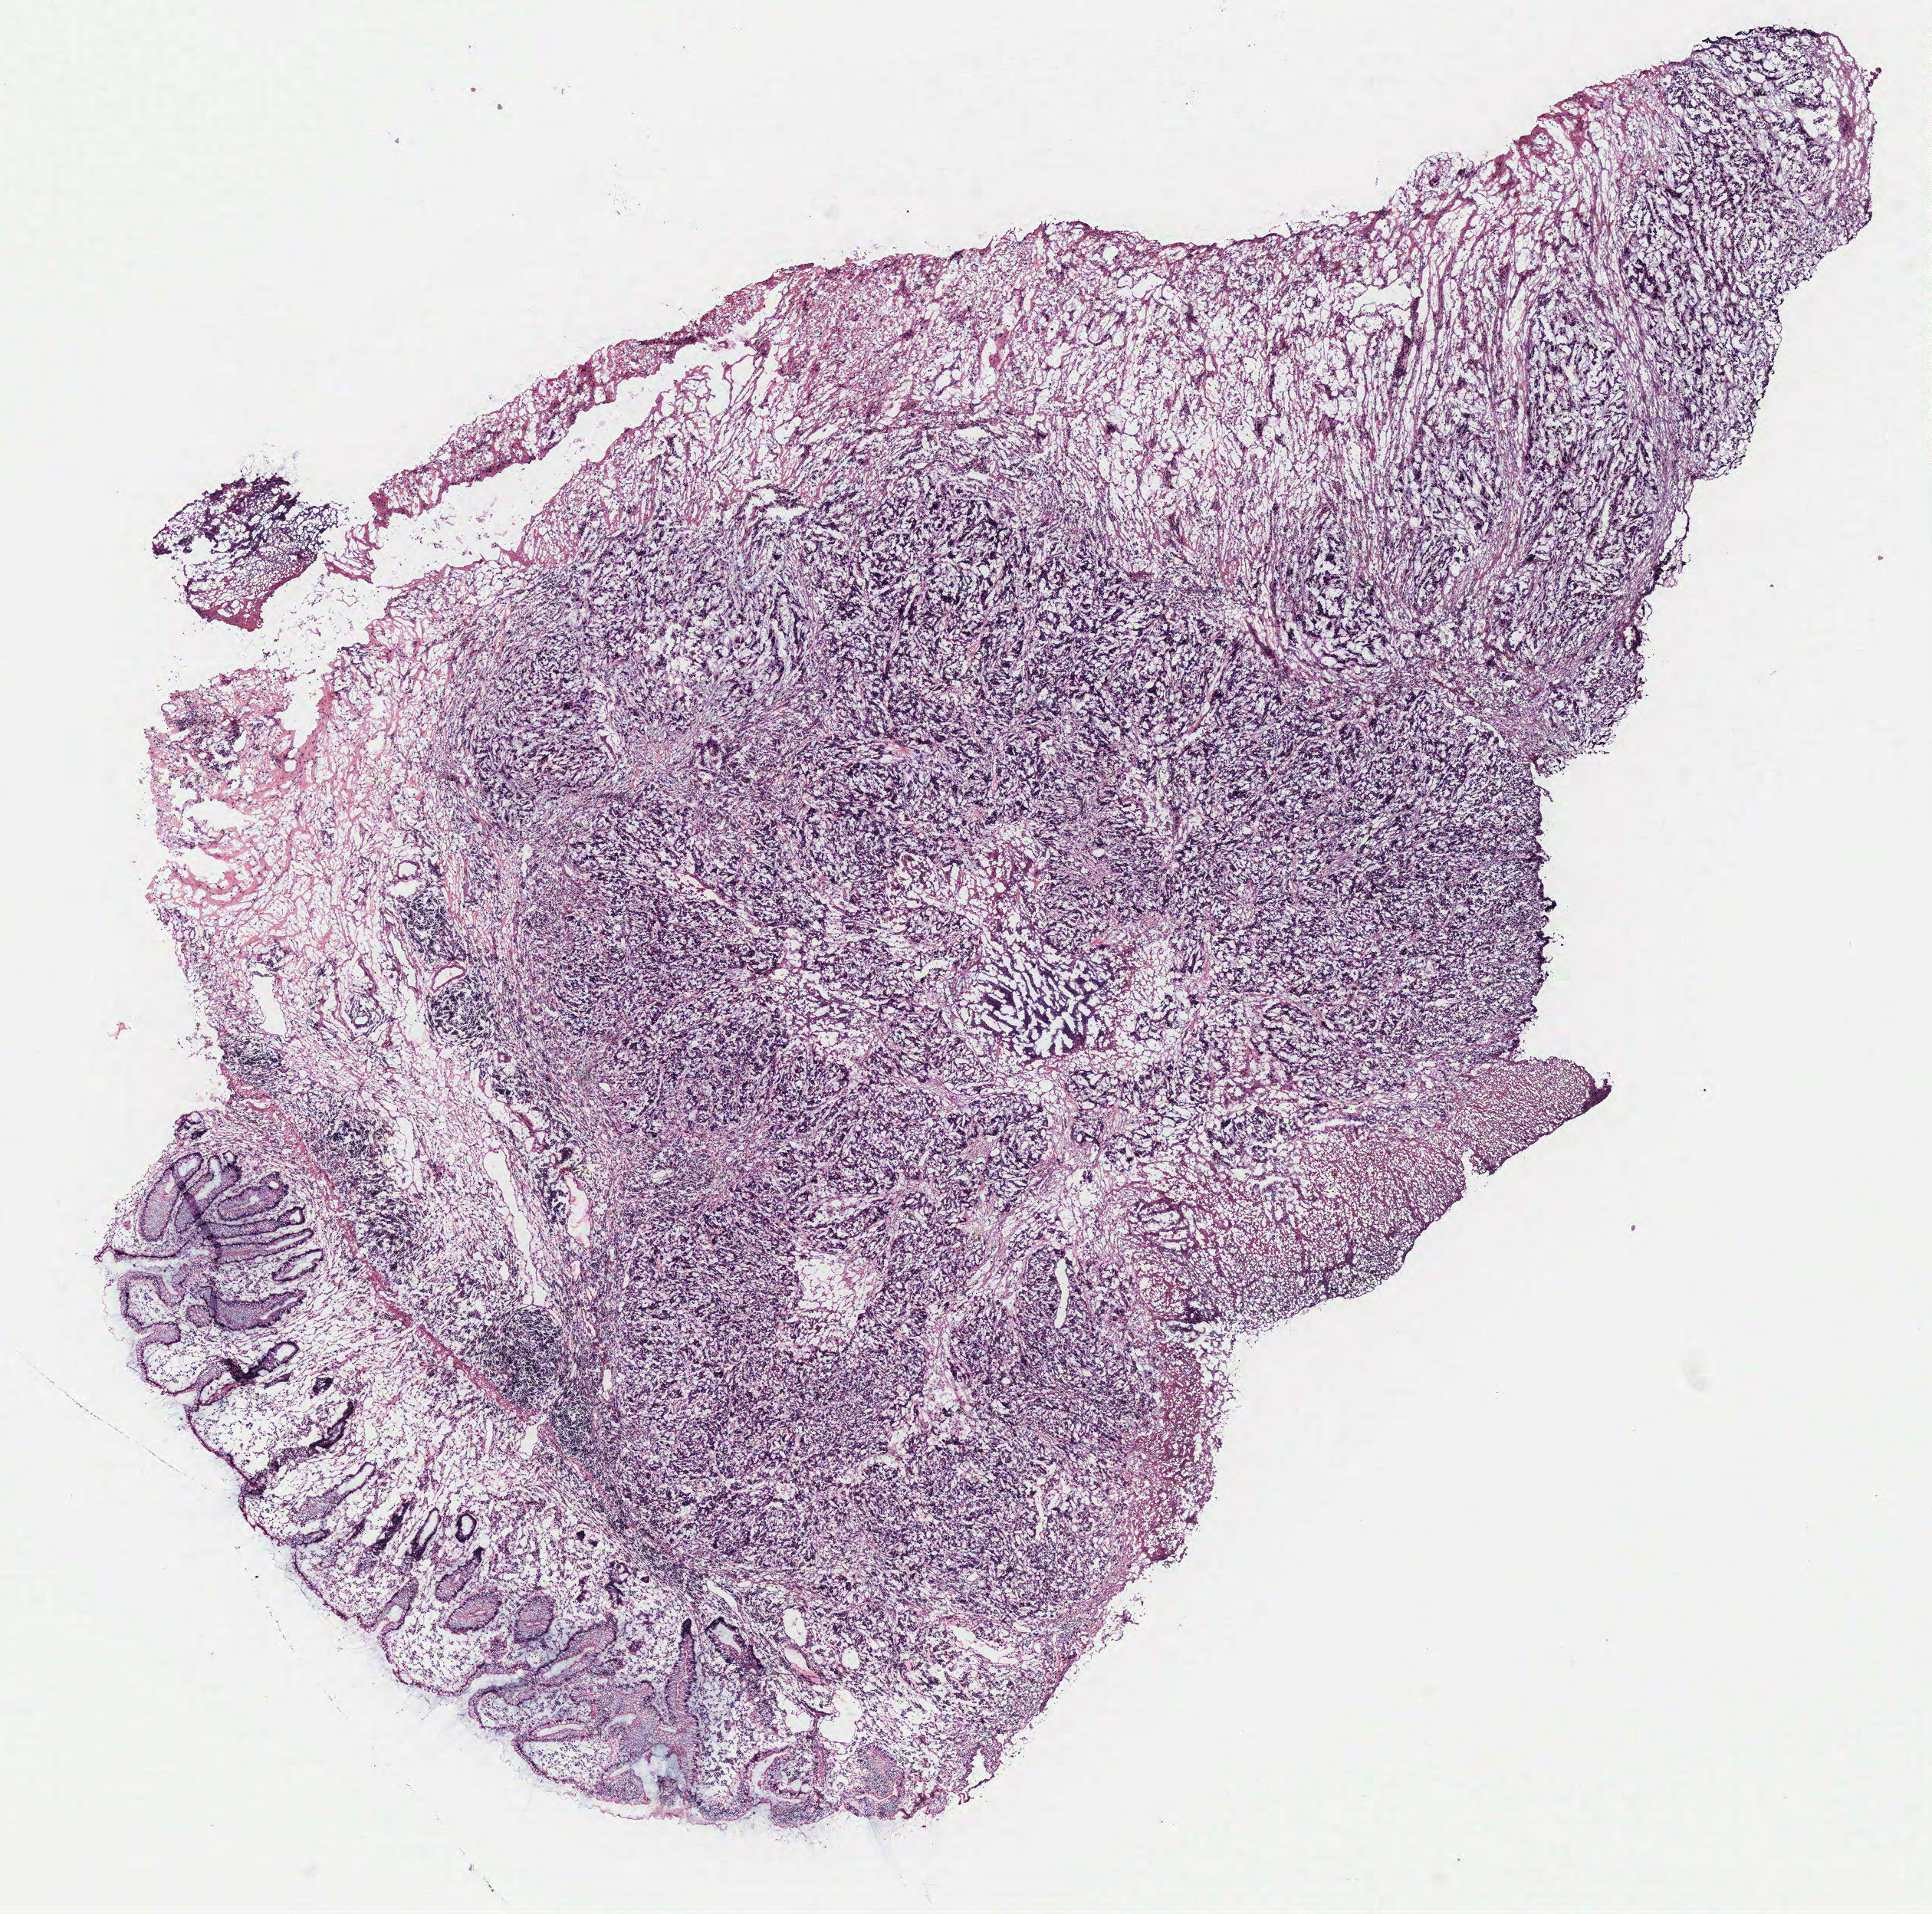
Digitized H&E tissue section (whole slide), shown as a low-resolution overview of the whole scanned area (about 10.1 x 10.0 mm, from a 40x scan). Normal (non-tumour) tissue sample, colon. Female, 73 y/o.
• this section: normal (non-tumour) tissue from the same patient
• patient diagnosis: Adenocarcinoma, NOS